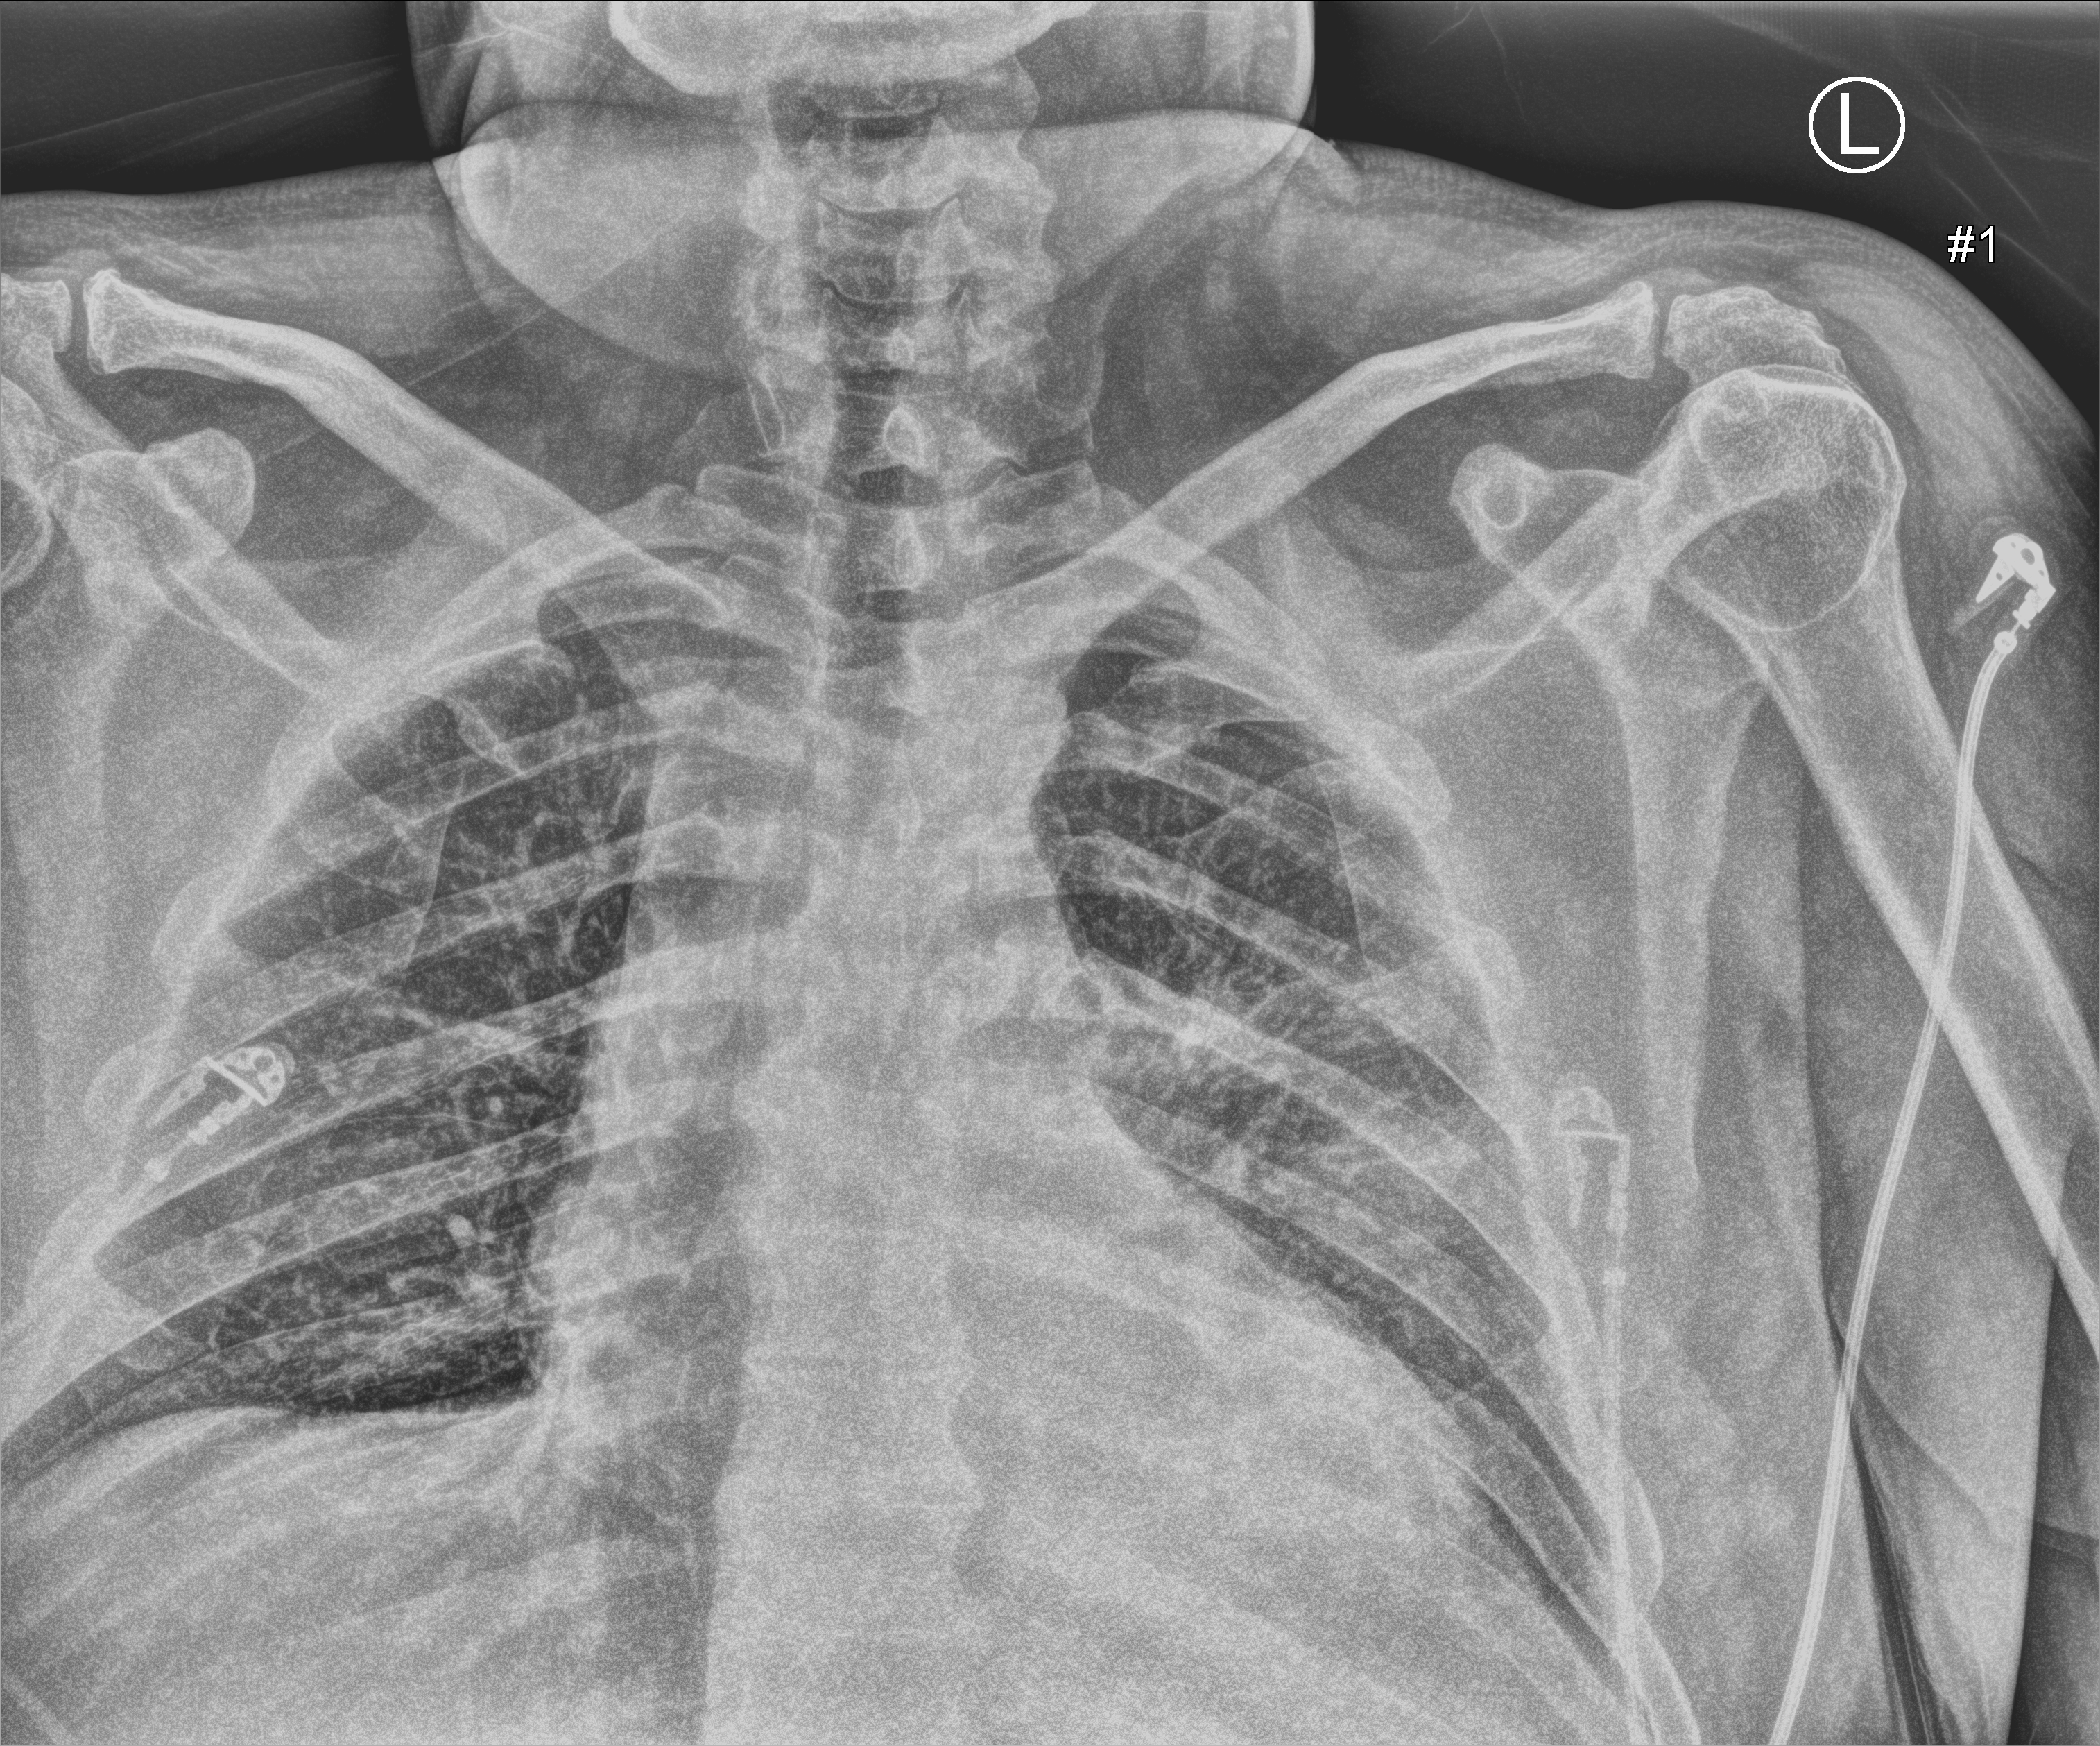
Portable chest radiograph; anteroposterior (AP) projection. Patient hospitalised with COVID-19; male, aged 18–59 years.
From the hospital-stay record, not from the radiograph (when in the stay this image was taken is not recorded): length of hospital stay: 10 days.